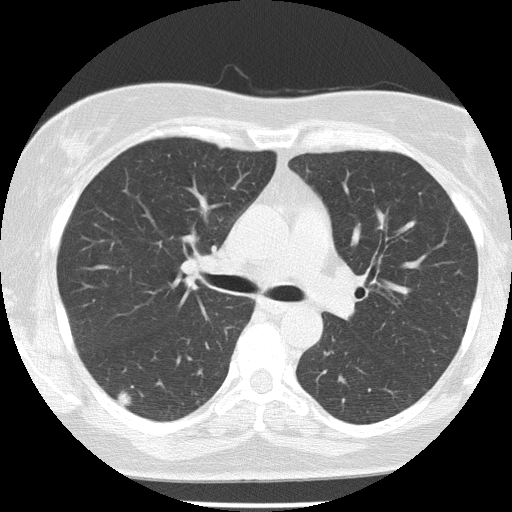
Axial slice from a low-dose chest CT screening exam; first (baseline) screen; lung window (W 1500 / L -600 HU); slice 59 of 142 in the series. Female, age 58 years at enrolment.
- Expert-annotated lung lesion, bounding box [x1, y1, x2, y2] px = [98, 372, 151, 423].
- The screening reader recorded 2 non-calcified nodules or masses ≥4 mm on this exam (right lower lobe, right lower lobe); which of them this box marks is not recorded.
- Later outcome: lung cancer diagnosed 648 days after this screen — adenocarcinoma, NOS, right lower lobe, well differentiated (G1), stage IB (AJCC 6th edition), 10 mm at pathology.